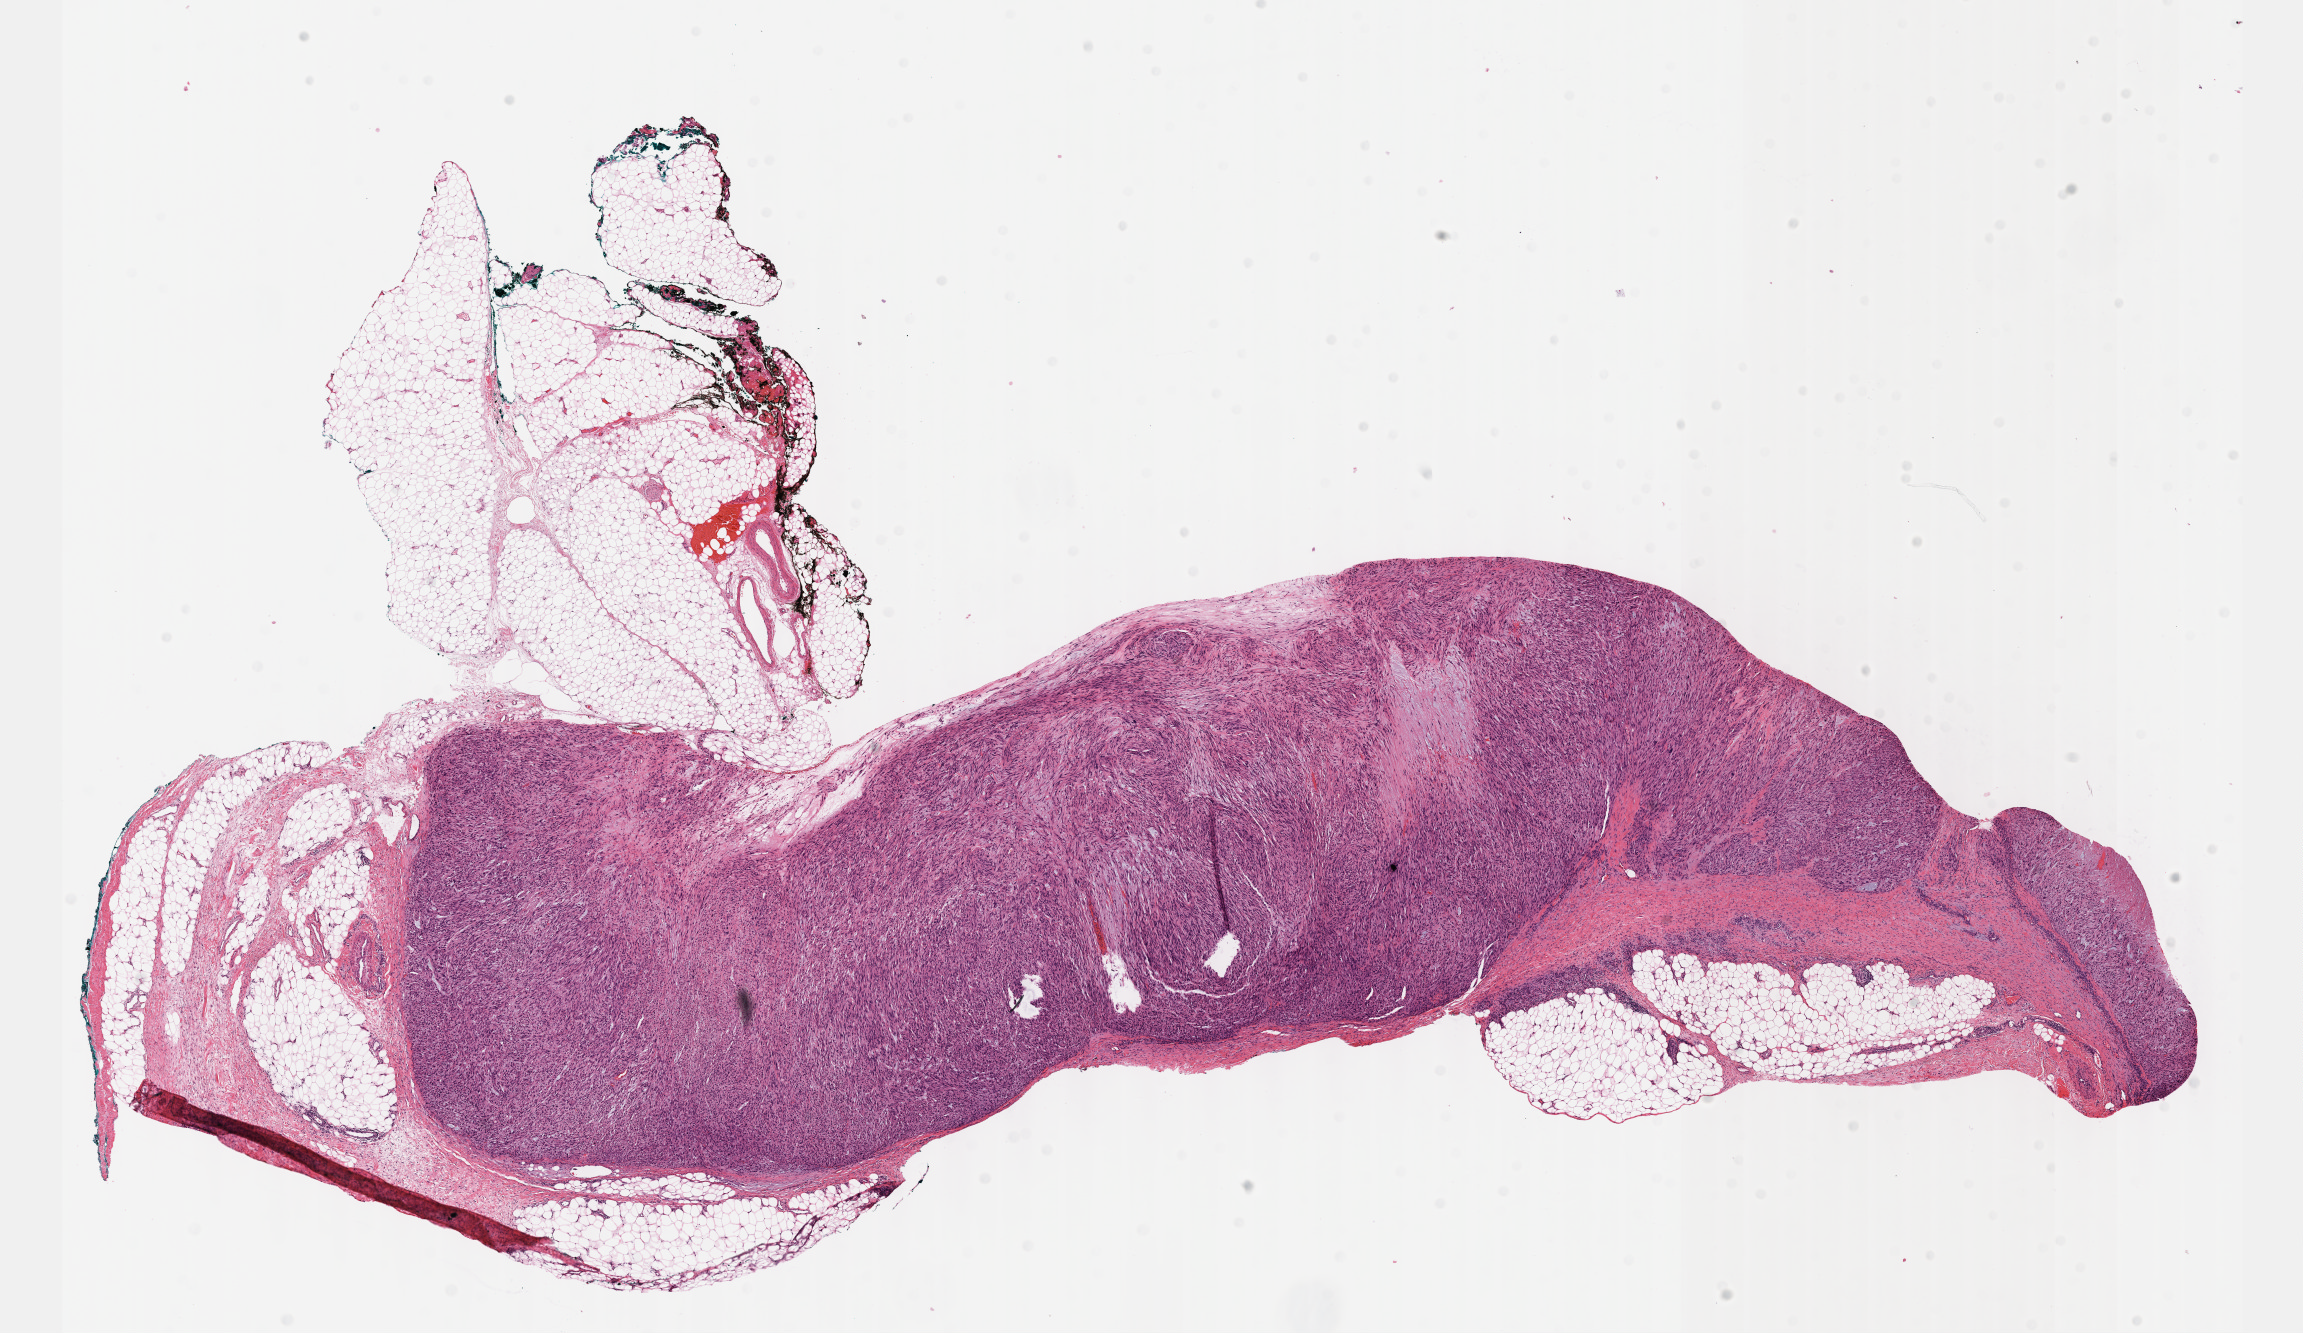
Digitized Hematoxylin and eosin (H&E) stained tissue section (whole slide) — whole scanned area (about 18.6 x 10.8 mm, from a 40x scan) shown as a low-resolution overview, FFPE section, primary tumour sample from the connective, subcutaneous and other soft tissues. Female, age 63 years at initial diagnosis.
Pathologic diagnosis: Leiomyosarcoma, NOS (connective, subcutaneous and other soft tissues of lower limb and hip).